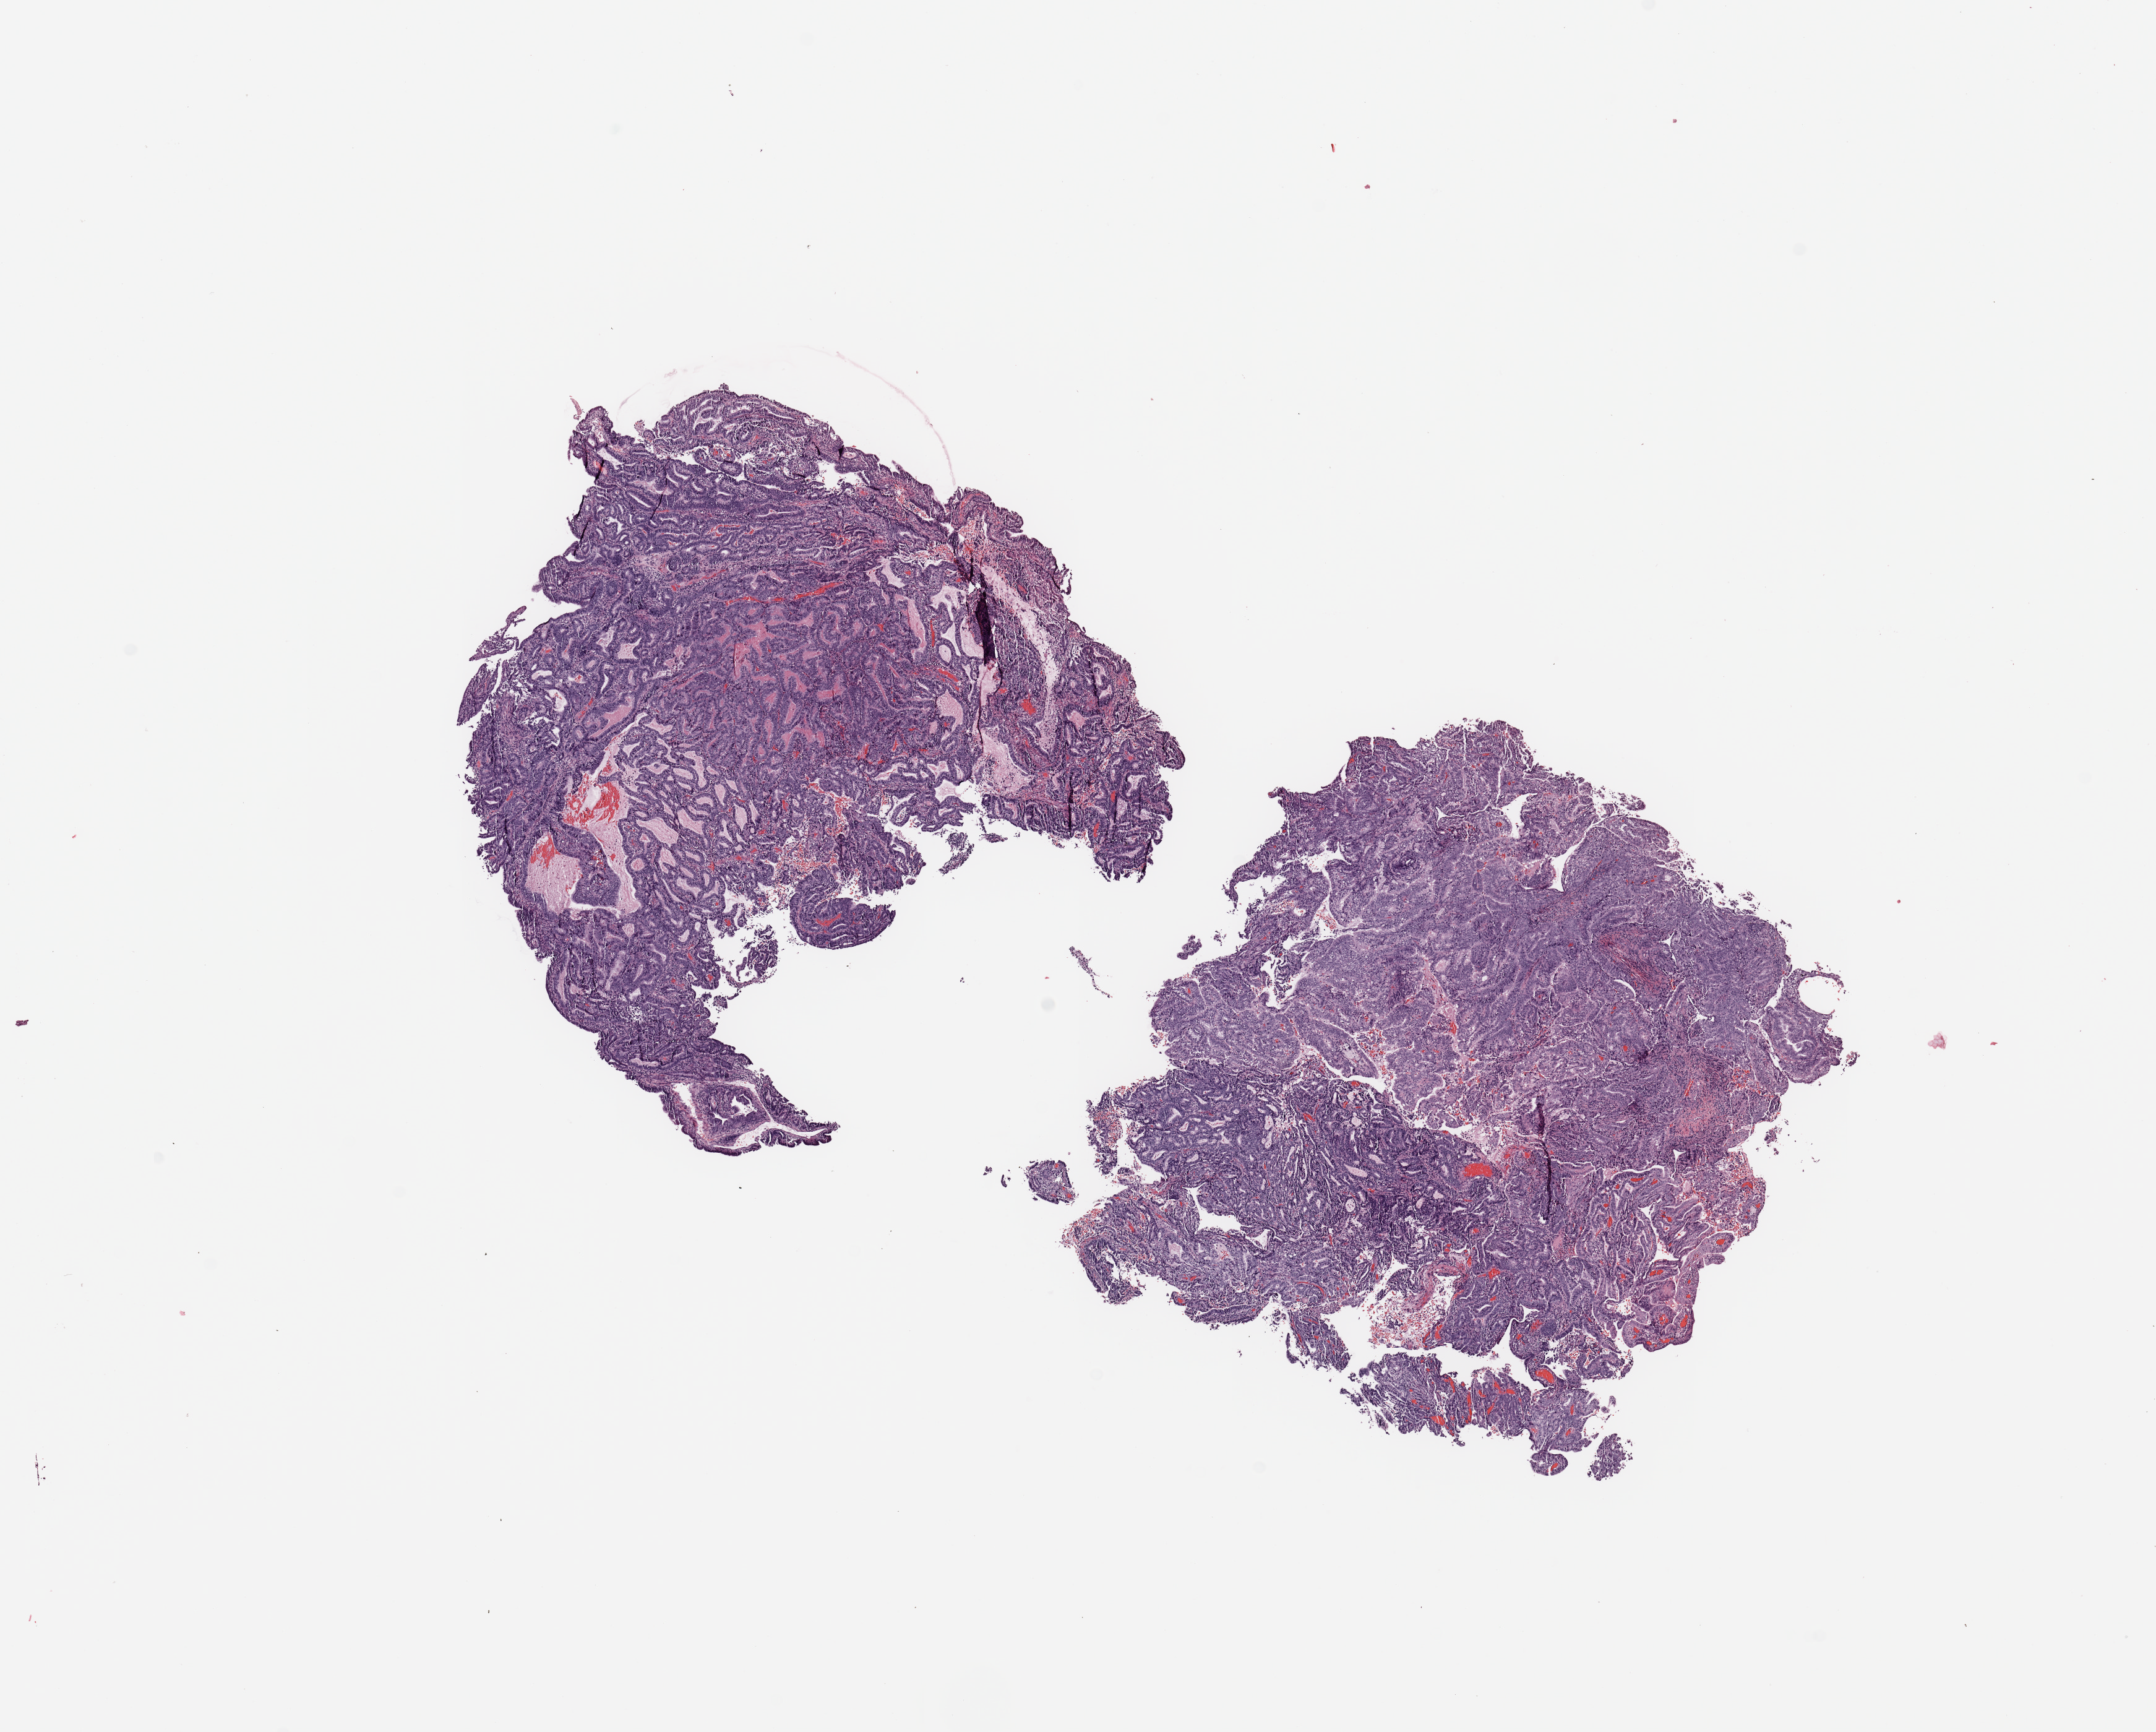
Digitized H&E tissue section (whole slide), low-resolution overview of the scanned area, about 13.8 x 11.1 mm (acquisition: 20x scan); tumour tissue sample, sampled site: uterus. 62-year-old female patient. Pathologist review of this section (percent, as recorded): tumour nuclei 90%, necrosis 0%.
Histologic diagnosis: Endometrioid adenocarcinoma, NOS.